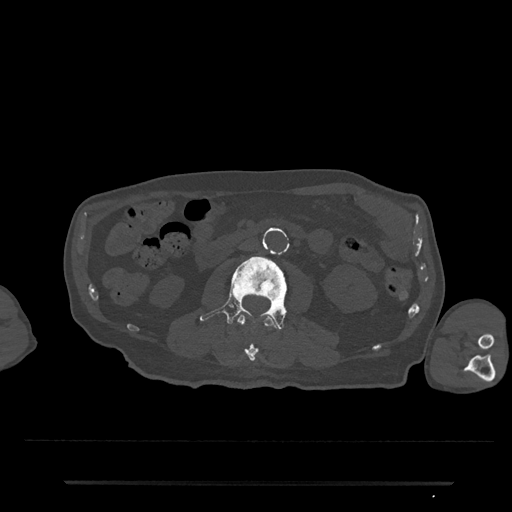
CT including the spine, one axial slice. Position 8 of 797 along the scan axis. Reconstruction kernel Br40s/3. 120 kVp. Bone window (W 1800 / L 400 HU). 0.5 mm slice thickness. 512 × 512 image matrix, field of view 427 × 427 mm. Patient: male, 74 years. Case-level facts recorded for this patient, not image findings: primary cancer: prostate.
Outlined on this slice (semi-automatically segmented with operator editing):
- L2 vertebra: bounding box <236,314,279,362> (left, top, right, bottom; pixels)
- L3 vertebra: <200,253,304,329>